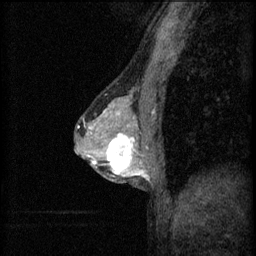
Breast MRI (dynamic contrast-enhanced), one sagittal slice. Slice 33 of 60 in the series (ordered by position). 3 images stored at this slice position (order not interpretable as contrast timing). 1.5 T. TE 4.2 ms, TR 8.2 ms. 256 × 256 image matrix. Female patient, age 44 years.
Structures marked on this image (semi-automatic segmentation, software-assisted and operator-edited):
- analysis volume of interest (the breast-tissue region the enhancement analysis was run in; not a lesion): bounding box (x1, y1, x2, y2) in pixels: (102, 132, 151, 181)
- tumour enhancement mask (voxels above the 70 % enhancement threshold inside the analysis volume of interest): (106, 134, 149, 177)